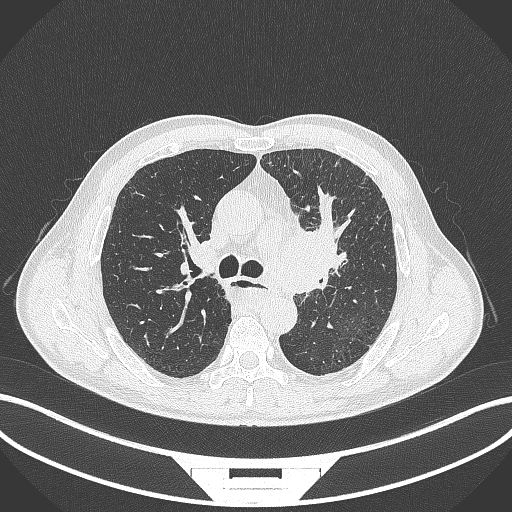
Chest CT, one axial slice. Position 247 of 411 along the scan axis. Reconstruction kernel B70f. 120 kVp. Lung window (W 1500 / L -600 HU). 1 mm slice thickness. 512 × 512 image matrix, field of view 400 × 400 mm. Patient: male, 57 years. From the clinical record (not read from this slice): clinical TNM (as recorded): T2a N1 M0.
Outlined on this slice (rectangle marked by the reading radiologist):
- lung tumour (recorded histology: squamous cell carcinoma): bounding box <271,211,360,303> (left, top, right, bottom; pixels)